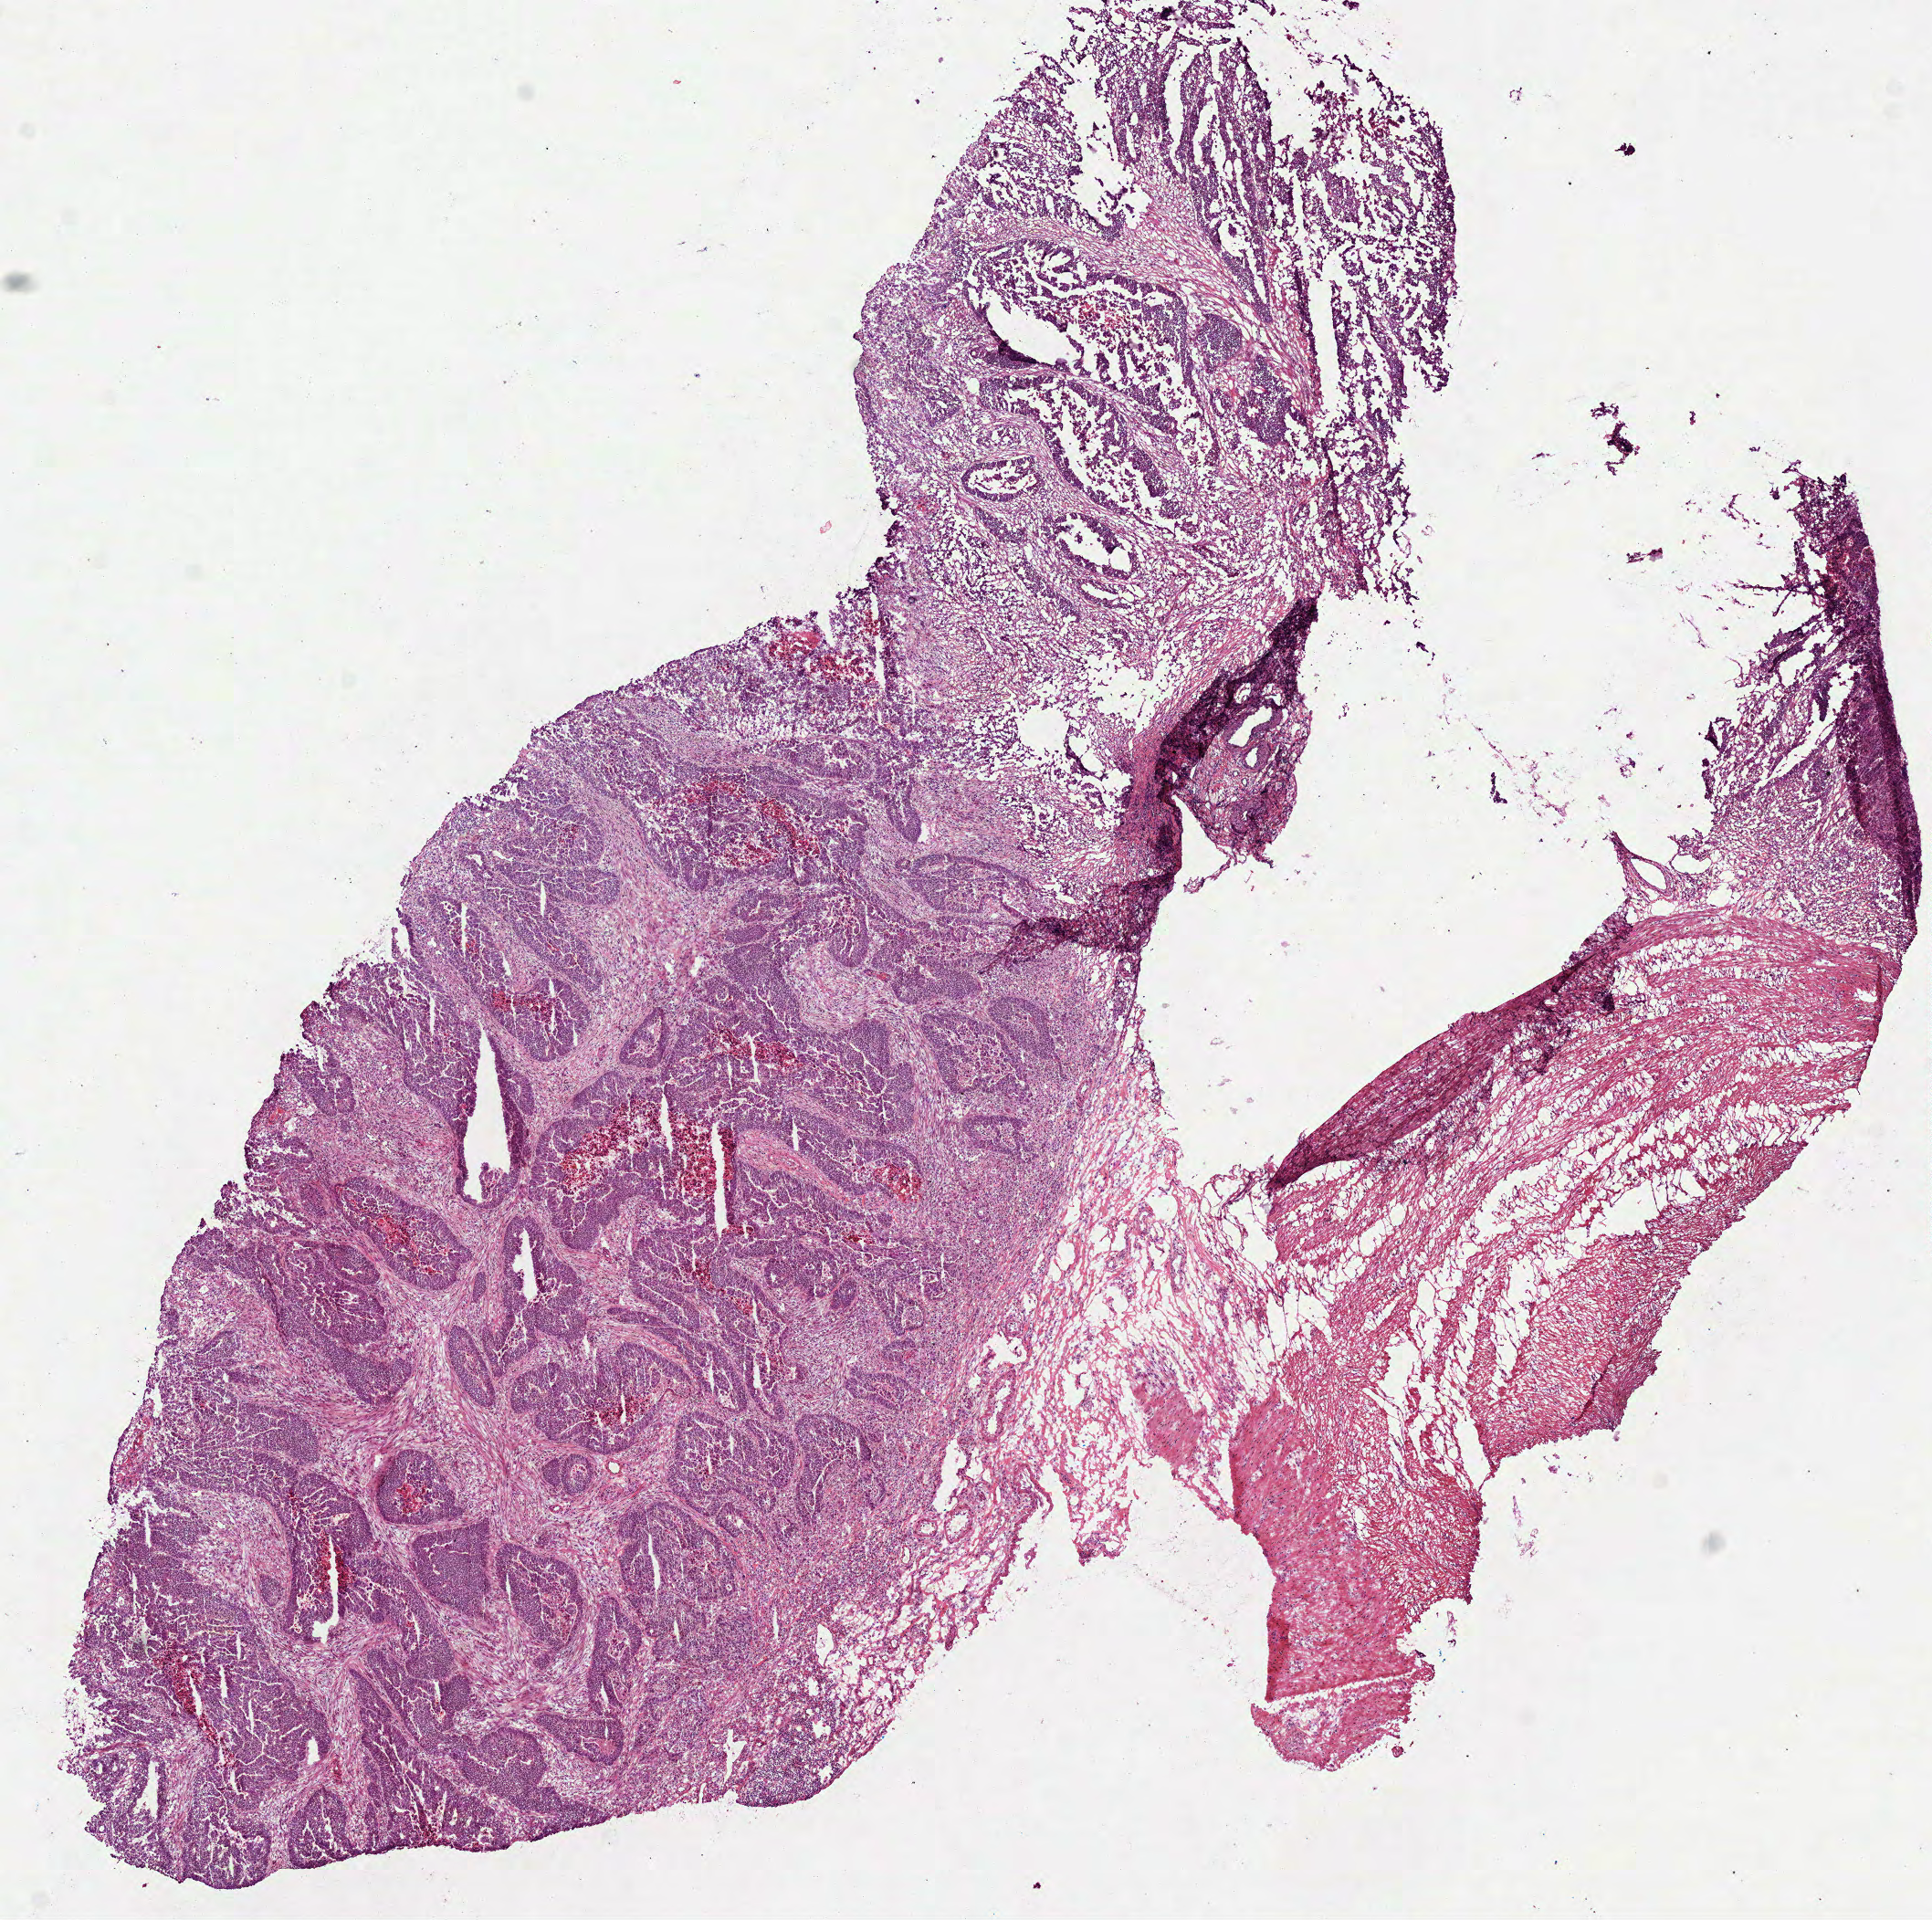
Hematoxylin and eosin (H&E) stained whole-slide image — a low-resolution overview of the entire scanned area, about 8.5 x 8.5 mm (acquisition: 40x scan); frozen section; primary tumour sample from the rectum. Male, age 73 years at initial diagnosis. Pathologist review of this section (percent, as recorded): tumour cells 60%, tumour nuclei 75%, normal cells 0%, stromal cells 25%, necrosis 15%.
Lymph nodes positive (case pathology): 0 of 15 examined. Diagnosis: Adenocarcinoma, NOS (rectosigmoid junction).